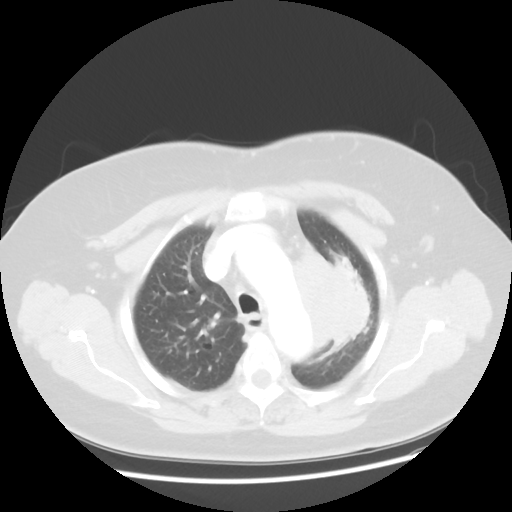
Chest CT, one axial slice; slice 36 of 49 in the series (ordered by position); reconstruction kernel STANDARD; 120 kVp; lung window (W 1500 / L -600 HU); 5 mm slice thickness; 512 × 512 image matrix. Female patient, age 58 years. From the clinical record (not read from this slice): clinical TNM (as recorded): T4 N3 M0.
Structures marked on this image (rectangle marked by the reading radiologist):
- lung tumour (recorded histology: small cell carcinoma): bounding box <289,243,375,352> (left, top, right, bottom; pixels)